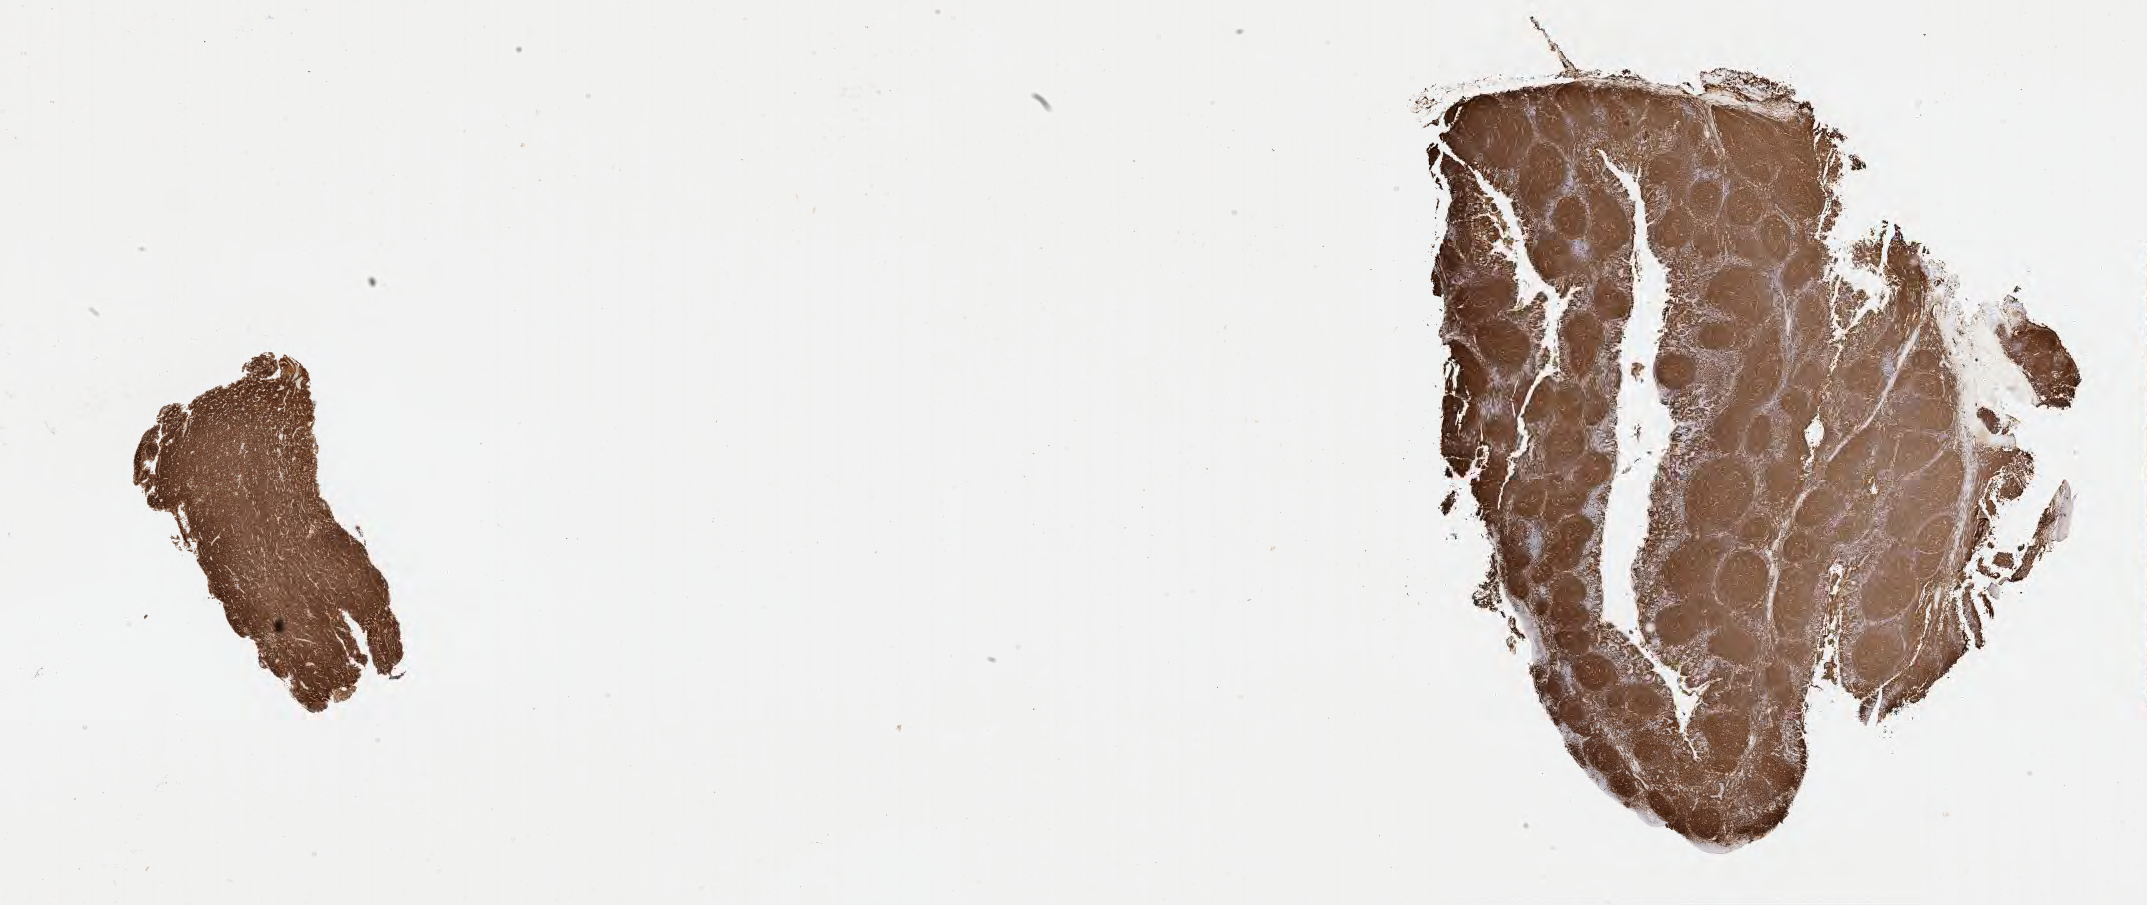
Whole-slide image, immunohistochemical stain for CD20, low-resolution overview of the scanned area, about 34.7 x 14.6 mm, specimen: tumor tissue, site: cranium. Patient: male, age 11 years.
* diagnosis: Diffuse large B-cell lymphoma, NOS